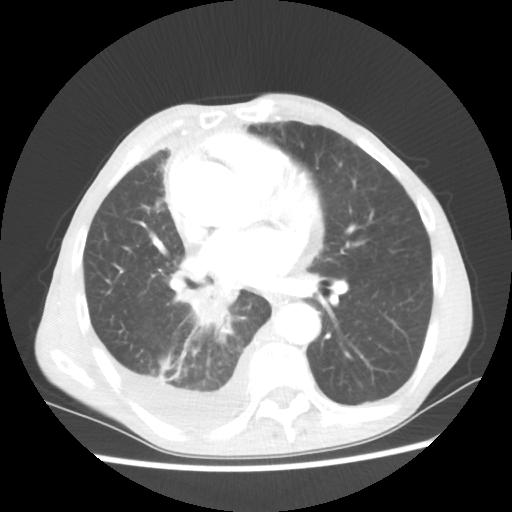
Chest CT, one axial slice. Slice 28 of 60 in the series (ordered by position). Reconstruction kernel STANDARD. 80 kVp. Lung window (W 1500 / L -600 HU). 512 × 512 image matrix, field of view 335 × 335 mm. Male patient, age 76 years. Case-level facts recorded for this patient, not image findings: clinical TNM (as recorded): T3 N3 M1a; histopathological grade: G3.
Structures marked on this image (bounding box drawn by a radiologist):
- lung tumour (recorded histology: squamous cell carcinoma): bounding box (x1, y1, x2, y2) in pixels: (169, 278, 240, 347)